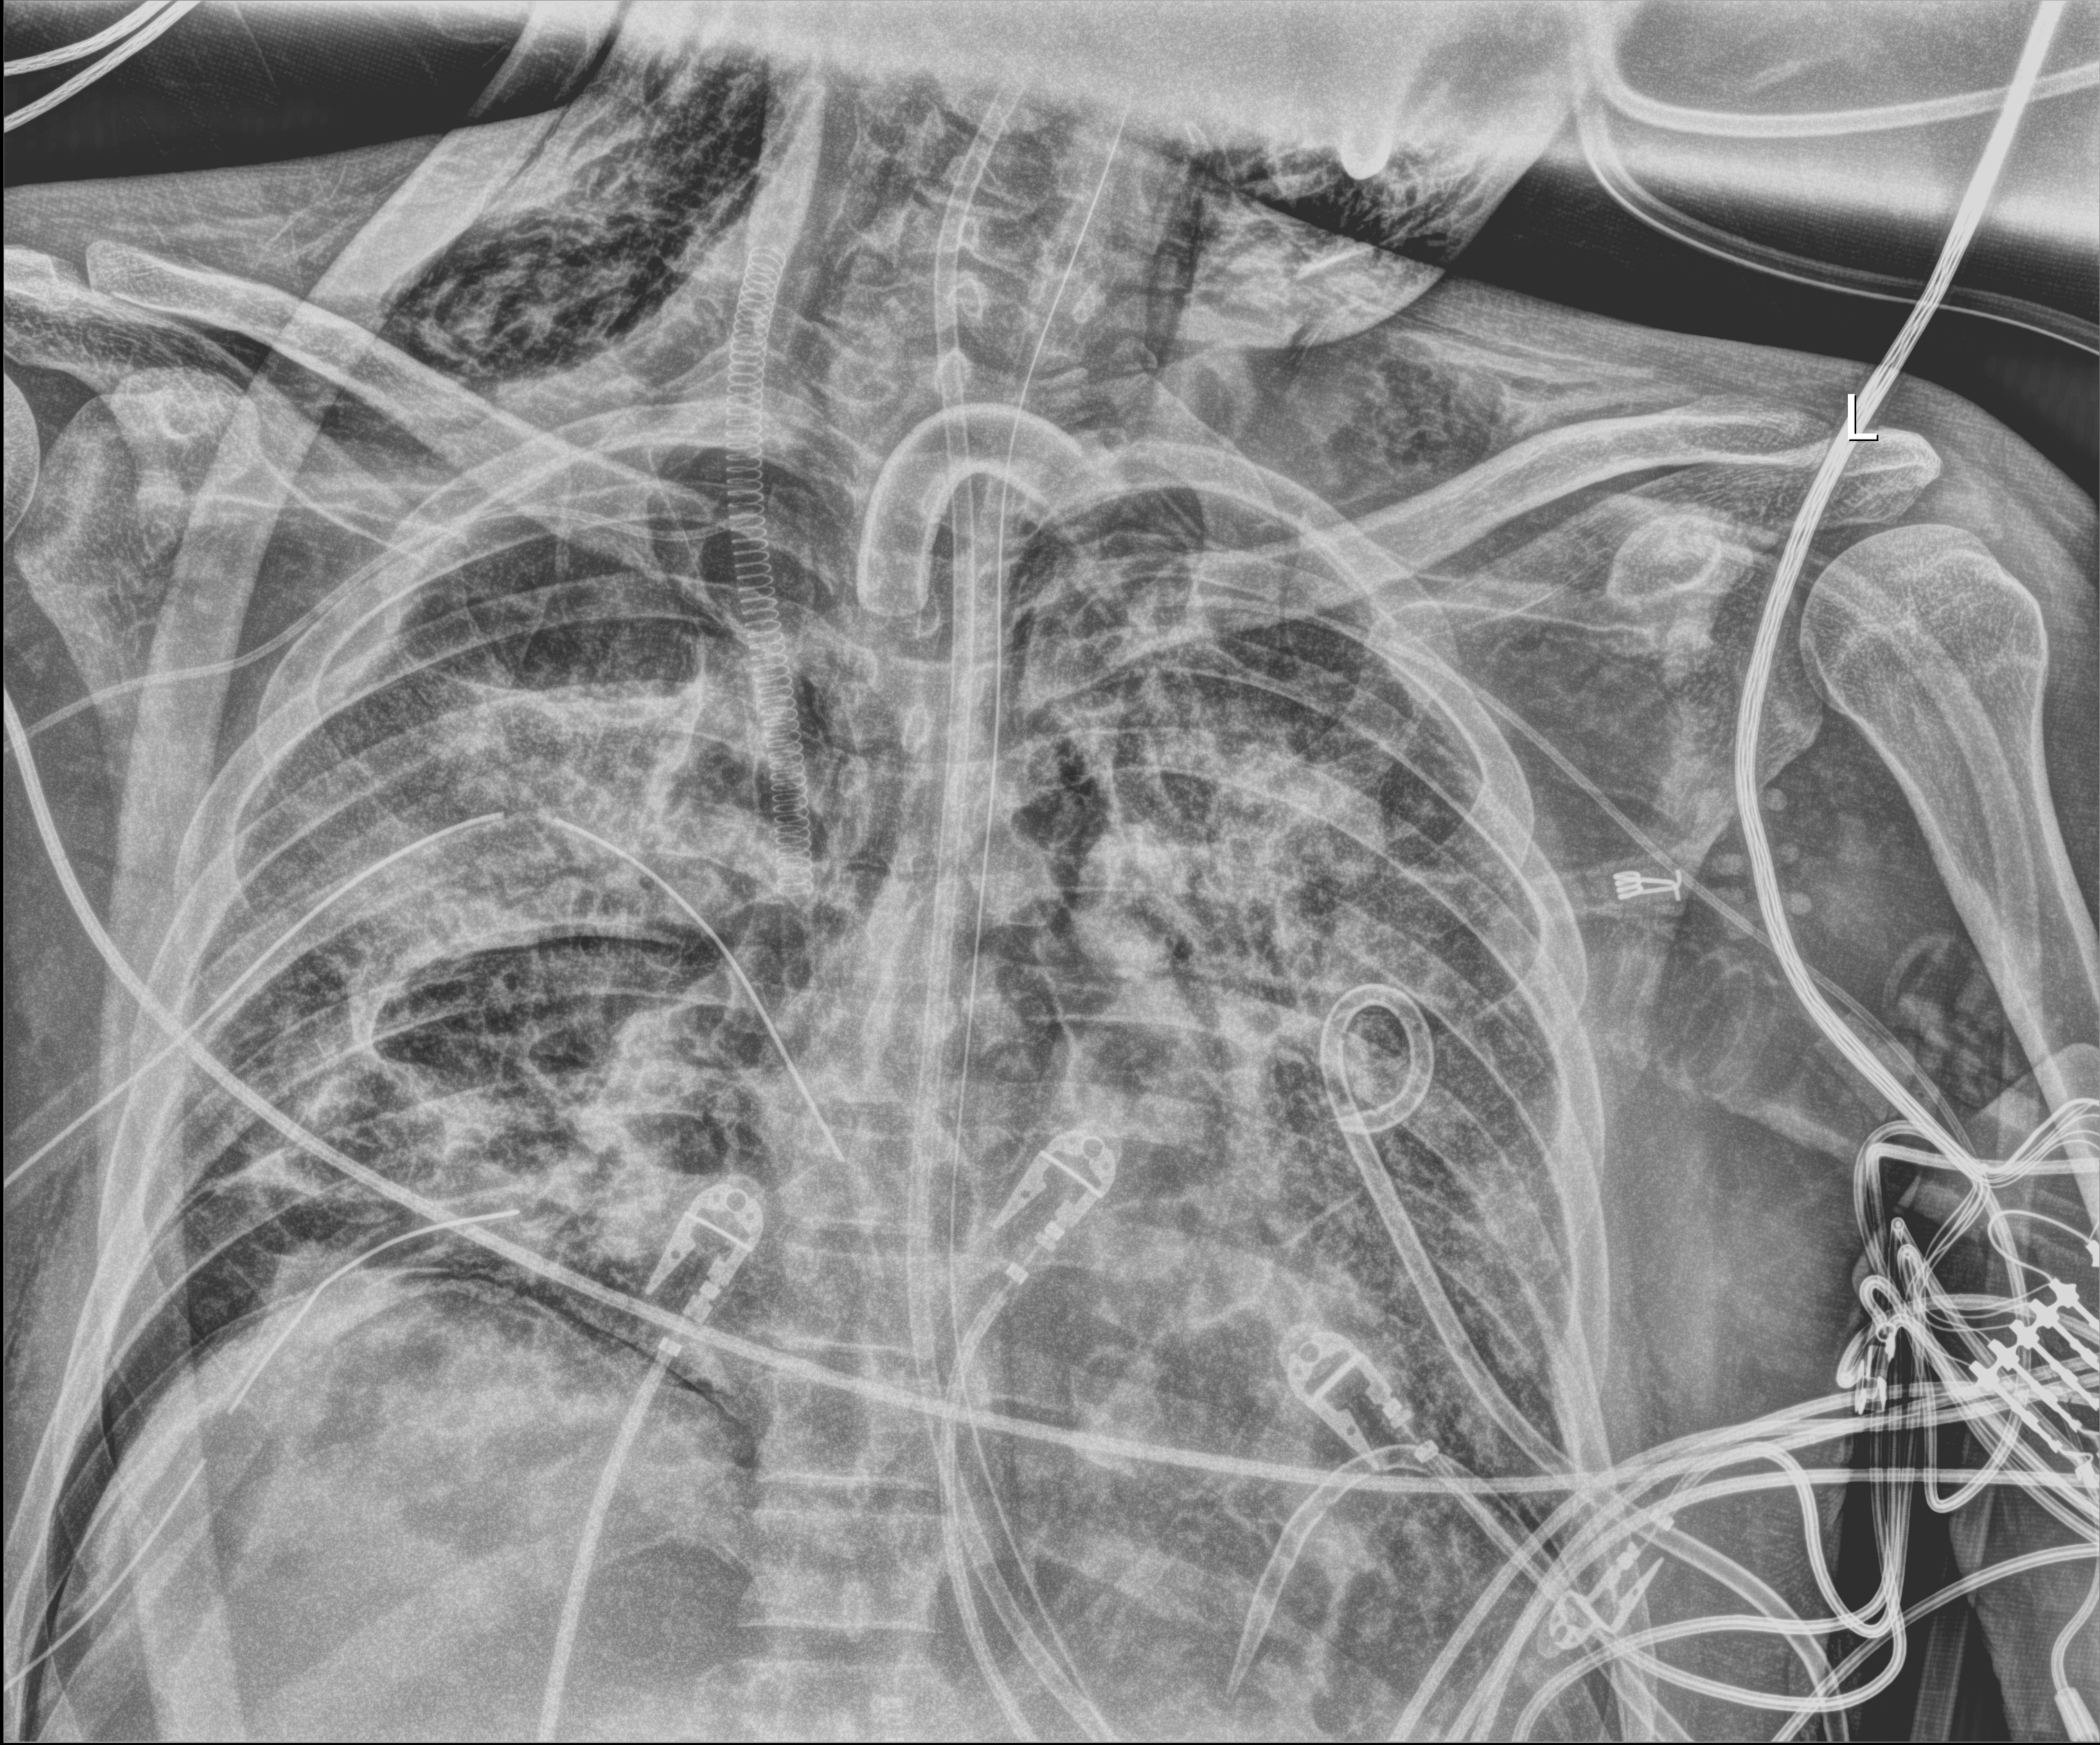
Chest radiograph (digital radiography). Patient hospitalised with COVID-19, aged 18–59 years.
Admission-level facts for this patient (not findings on this image; timing relative to this image not recorded):
- length of hospital stay: 60 days
- COPD (admission record): no